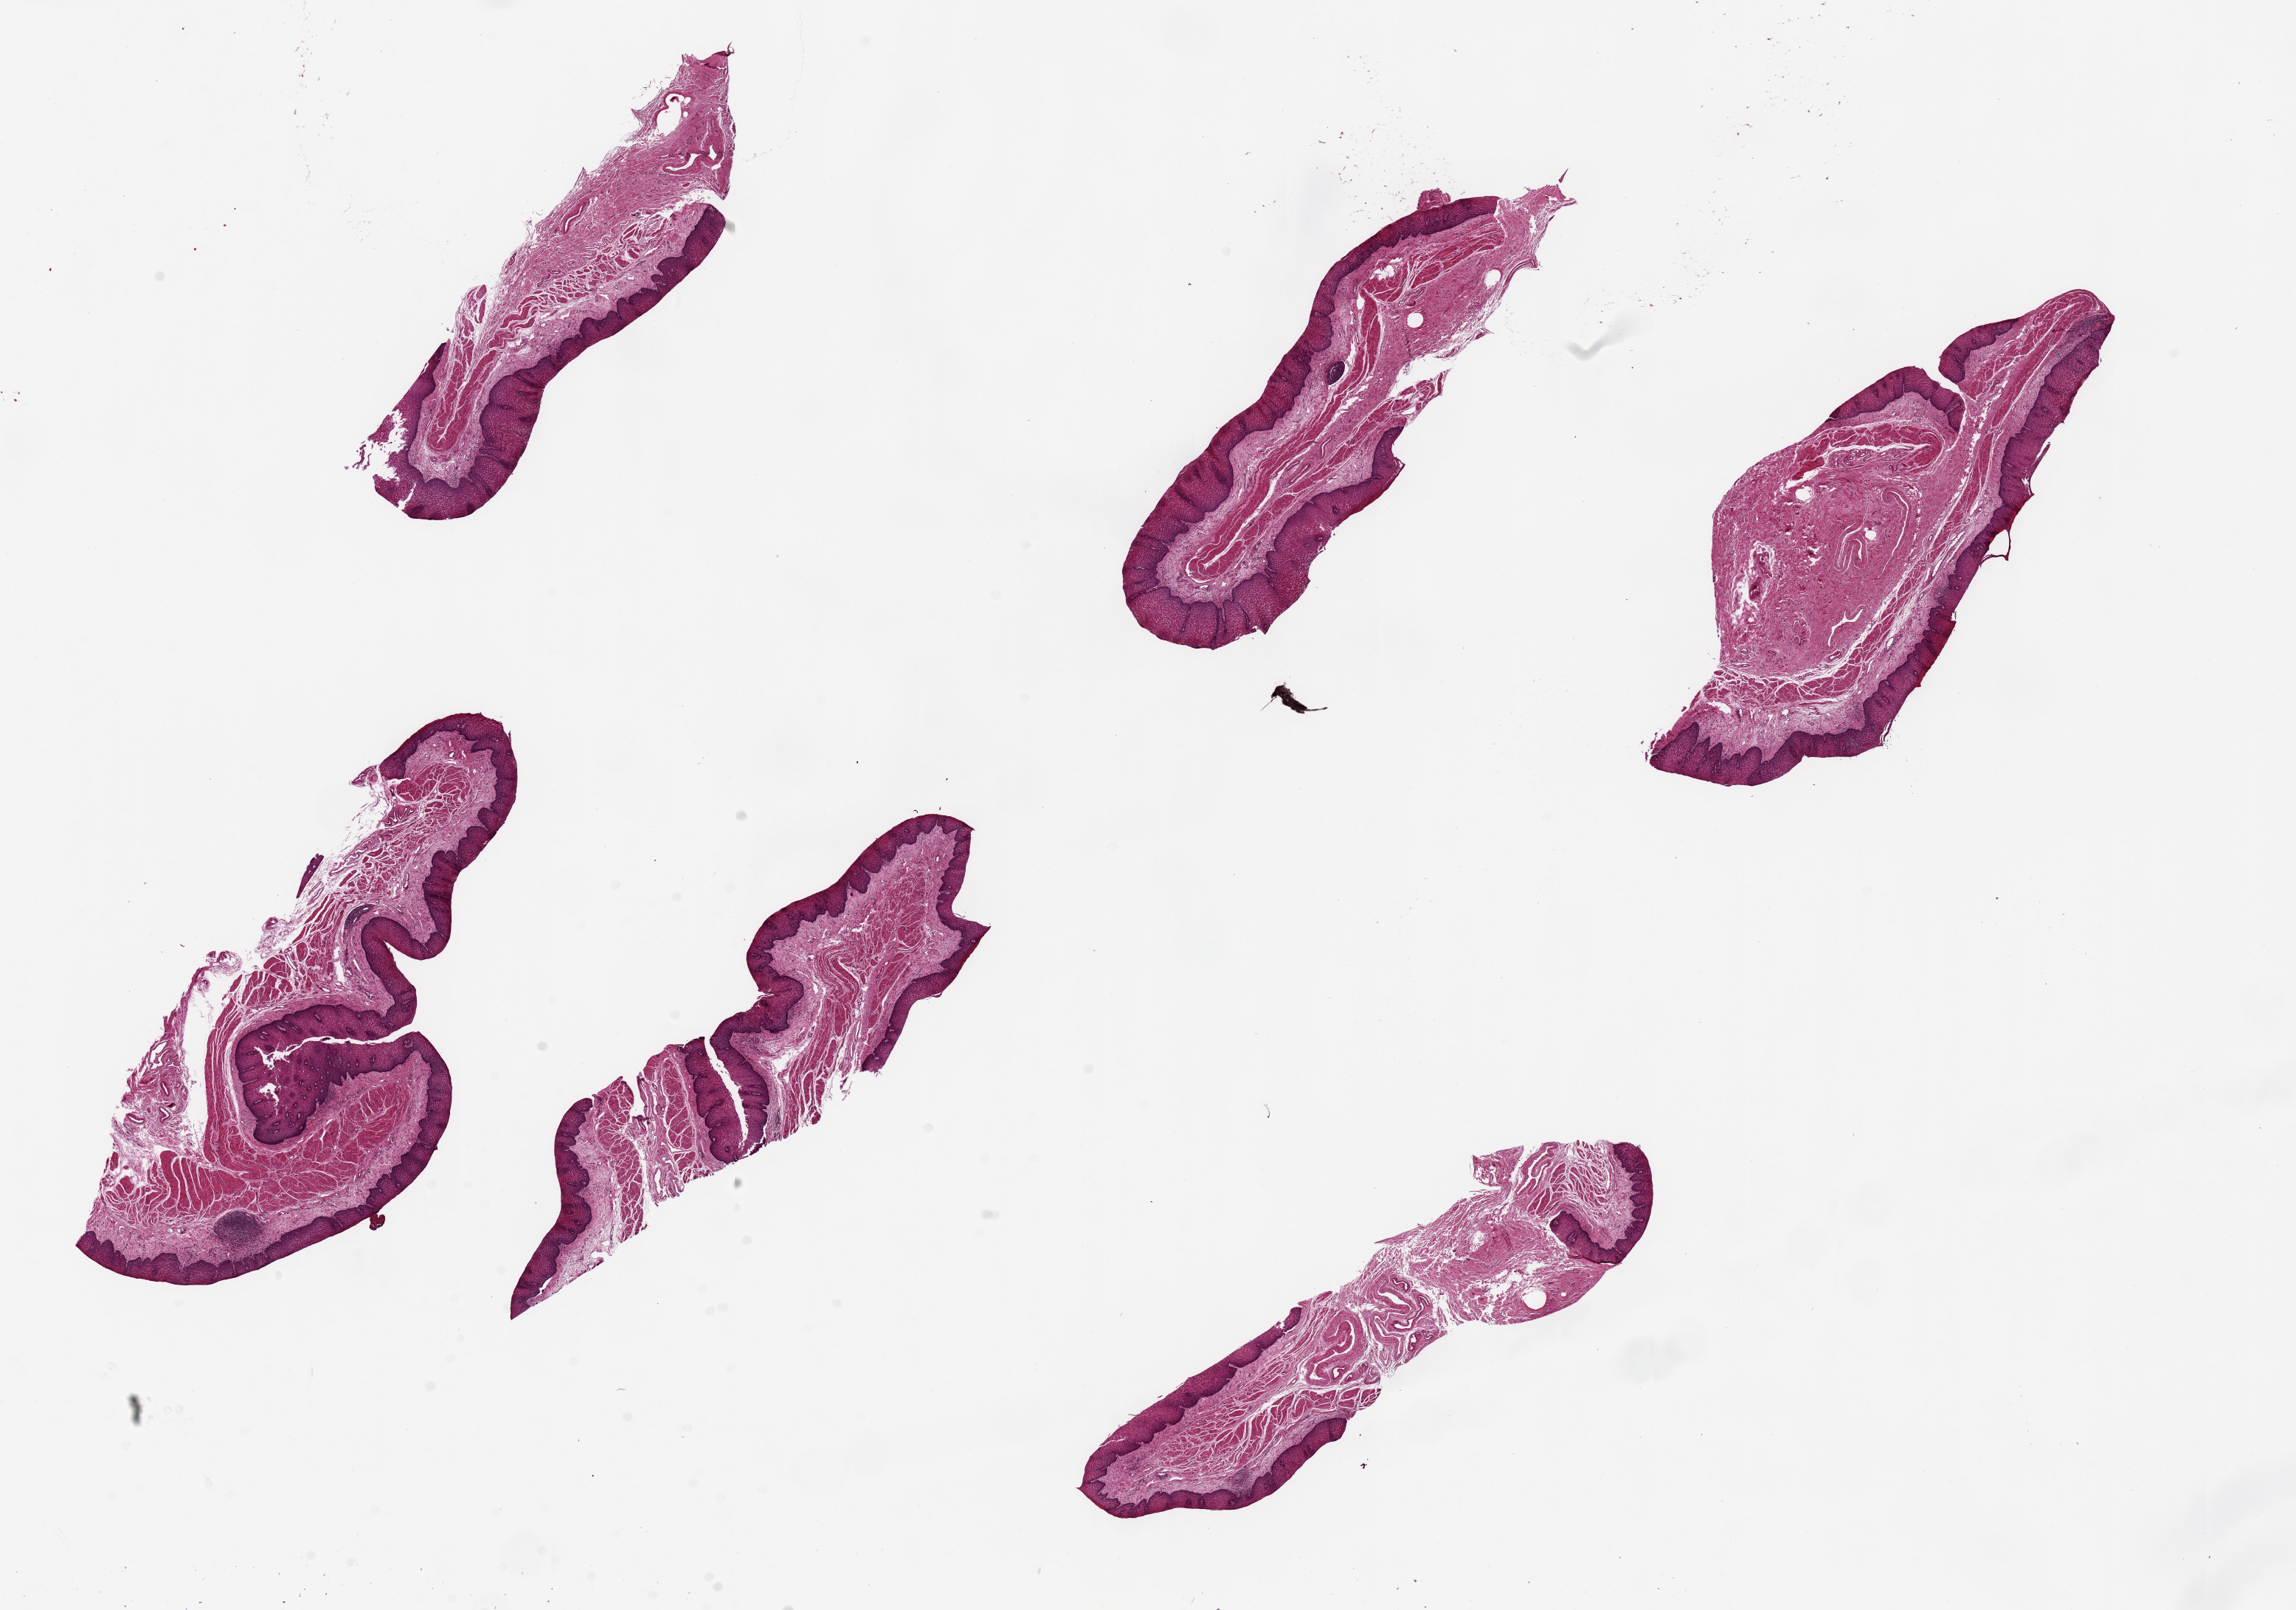
Haematoxylin and eosin whole-slide image, low-resolution overview of the scanned area, about 24.6 x 17.3 mm (from a 20x scan), PAXgene-fixed, paraffin-embedded tissue, section of esophageal mucous membrane (target tissue), tissue donor sample. Donor: female.
- pathologist's review note for this sample: 6 pieces, up to 7x3mm; ~20-30% thickness is well preserved squamous mucosa